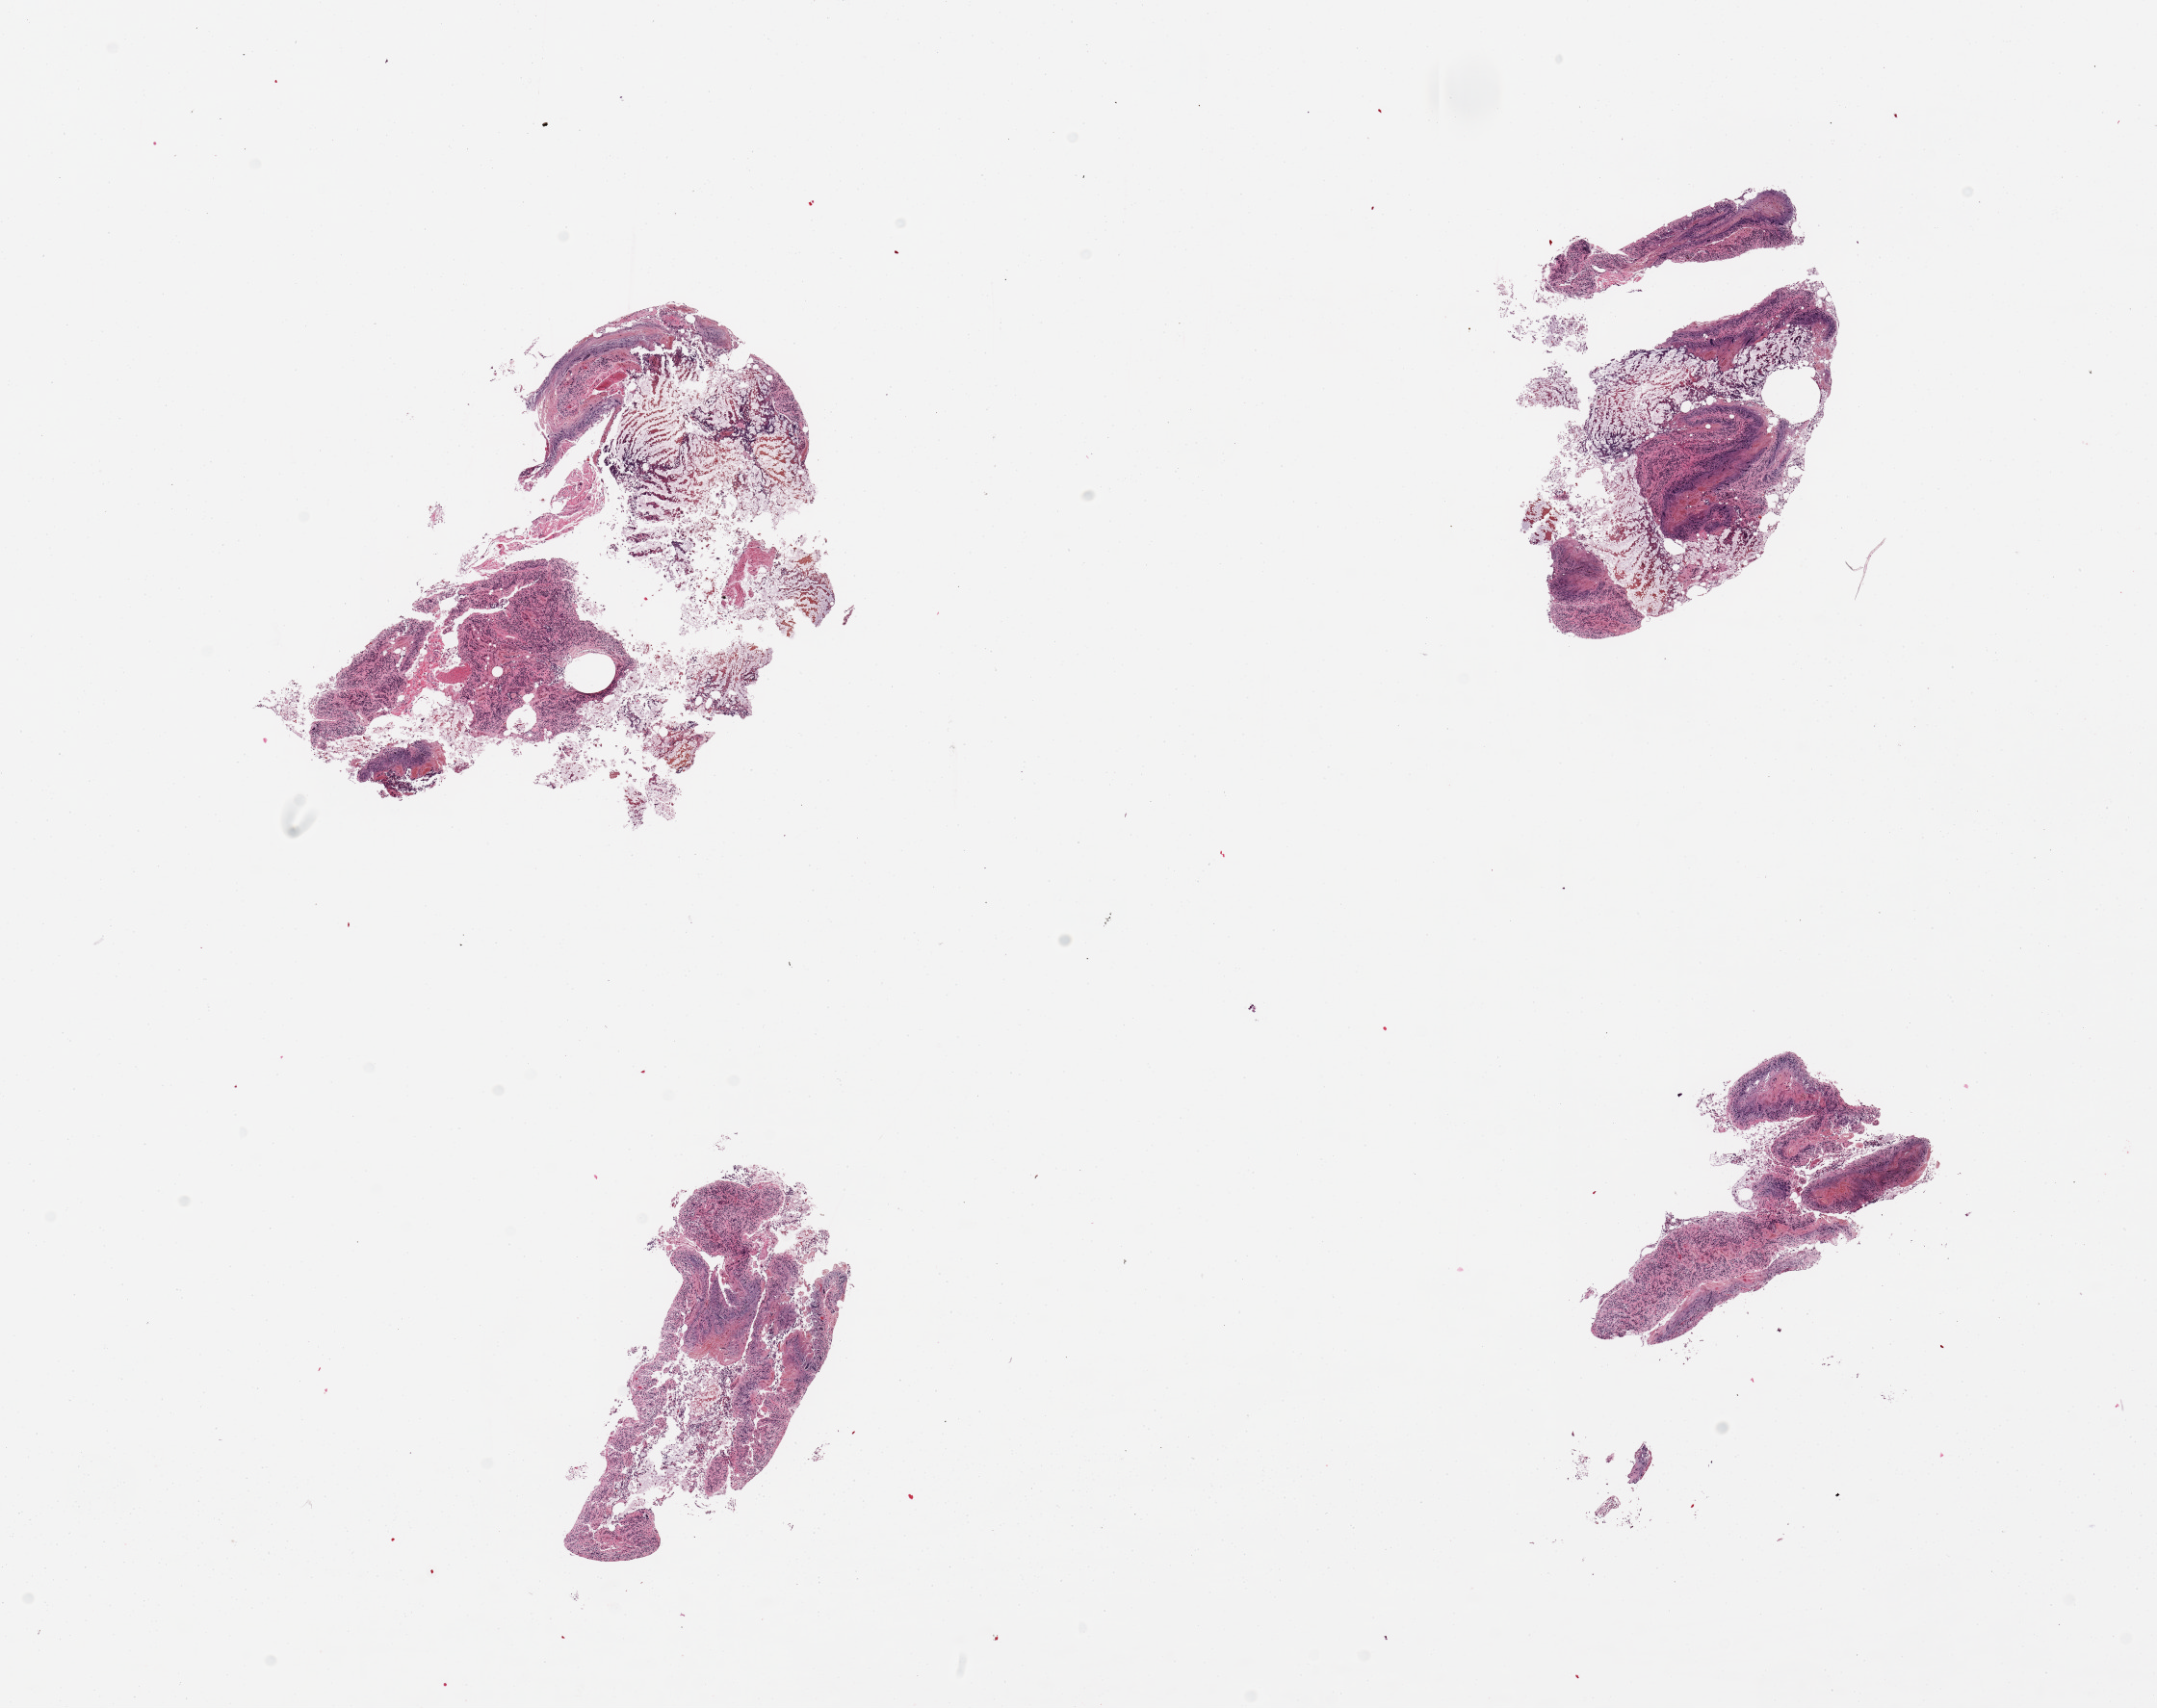
Digitized hematoxylin and eosin (H&E)-stained section, brightfield — whole scanned area (about 17.7 x 14.0 mm) shown as a low-resolution overview; PAXgene-fixed, paraffin-embedded tissue; sampled site (target tissue): ileum; tissue donor sample. Male donor.
Review note (as recorded): 4 pieces, ~20% residual lymphoid aggregates.